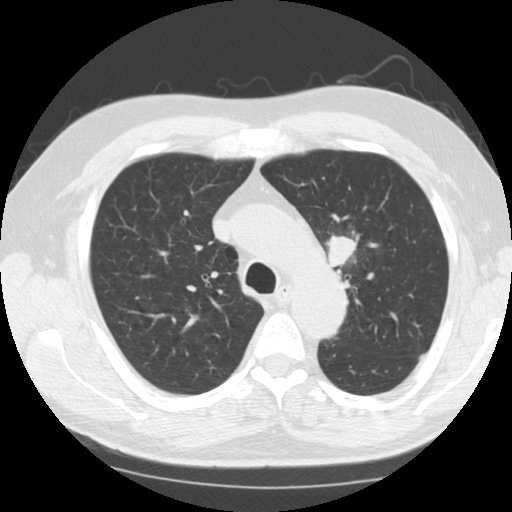
Low-dose screening chest CT, one axial slice. Slice 92 of 124 in the series (ordered by position). Lung window (W 1500 / L -600 HU). 512 × 512 image matrix, field of view 340 × 340 mm.
Annotated regions visible in this slice (manually delineated by an expert):
- lesion 1 (tumor, upper lobe of left lung): box from (x=327, y=232) to (x=357, y=268) px